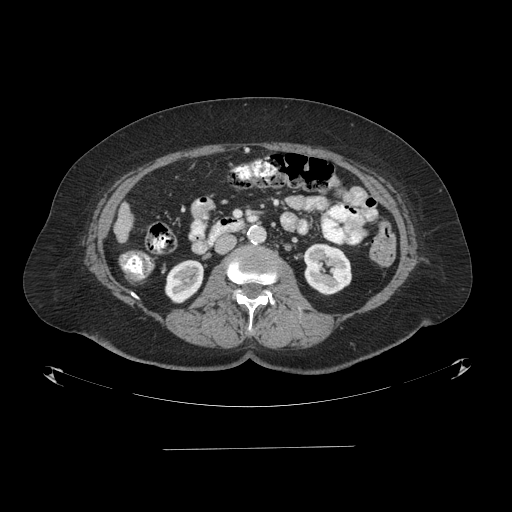
Contrast-enhanced abdominal CT (liver protocol), one axial slice; slice 17 of 103 in the series (ordered by position); reconstruction kernel STANDARD; 120 kVp; one of 2 acquisitions stored at this slice position; soft-tissue window (W 400 / L 40 HU); 2.5 mm slice thickness; 512 × 512 image matrix, field of view 500 × 500 mm. Case-level facts recorded for this patient, not image findings: diagnosis: hepatocellular carcinoma (patient treated with transarterial chemoembolisation; whether this scan precedes or follows treatment is not stated here); TNM stage (as recorded): Stage-IIIA; Child-Pugh class: A; tumour nodularity: multinodular; tumour size: 5.2 cm.
Annotated regions visible in this slice (semi-automatic segmentation, software-assisted and operator-edited):
- liver parenchyma outside the tumour (the mass and vessels are separate outlines, so this box may not span the whole liver): bounding box <114,203,132,242> (left, top, right, bottom; pixels)